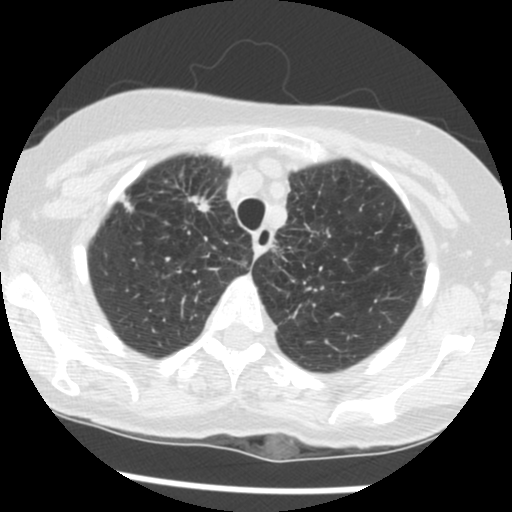
Axial slice from a low-dose chest CT screening exam; second annual screen; lung window (W 1500 / L -600 HU); 2.5 mm slice thickness; standard (soft-tissue) reconstruction kernel (STANDARD); 512 × 512 image matrix, field of view 290 × 290 mm. Female participant, aged 70 years at enrolment.
Expert reader's lesion annotation, bounding box <158,178,223,232> (left, top, right, bottom; pixels). Screening reader's record for this exam (one nodule recorded; not confirmed to be the boxed lesion): non-calcified nodule or mass ≥4 mm, right upper lobe, 11 × 7 mm, spiculated (stellate) margins, soft tissue attenuation, pre-existing on the prior screen: yes; interval growth: yes. Official screen result: positive, other.